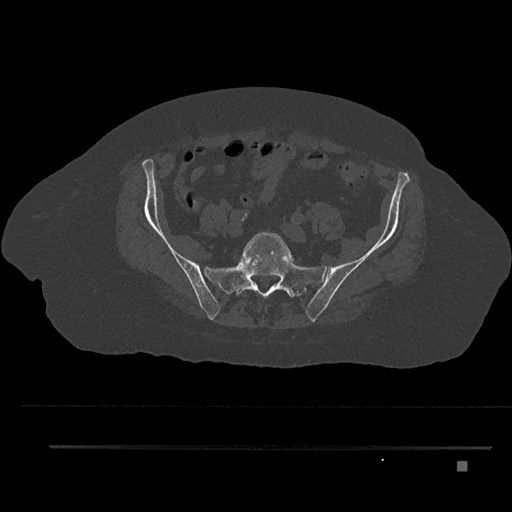
CT including the spine, one axial slice. Slice 12 of 797 in the series (ordered by position). Bone window (W 1800 / L 400 HU). 0.5 mm slice thickness. 512 × 512 image matrix. Patient: female, 76 years. From the clinical record (not read from this slice): primary cancer: lung; vertebrae with lytic lesions (as recorded): T11, L3.
Structures marked on this image (semi-automatically segmented with operator editing):
- L5 vertebra: bounding box <243,232,291,297> (left, top, right, bottom; pixels)